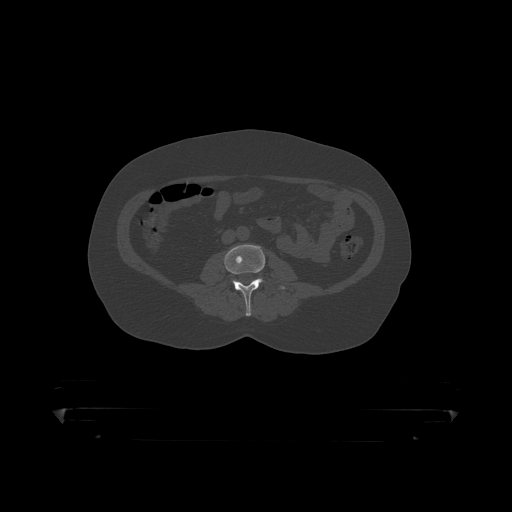
CT including the spine, one axial slice; position 86 of 390 along the scan axis; bone window (W 1800 / L 400 HU); 1.25 mm slice thickness; 512 × 512 image matrix. Male patient, age 60 years. From the clinical record (not read from this slice): primary cancer: prostate.
Structures marked on this image (semi-automatically segmented with operator editing):
- L3 vertebra: bounding box [x1, y1, x2, y2] px = [224, 245, 287, 317]